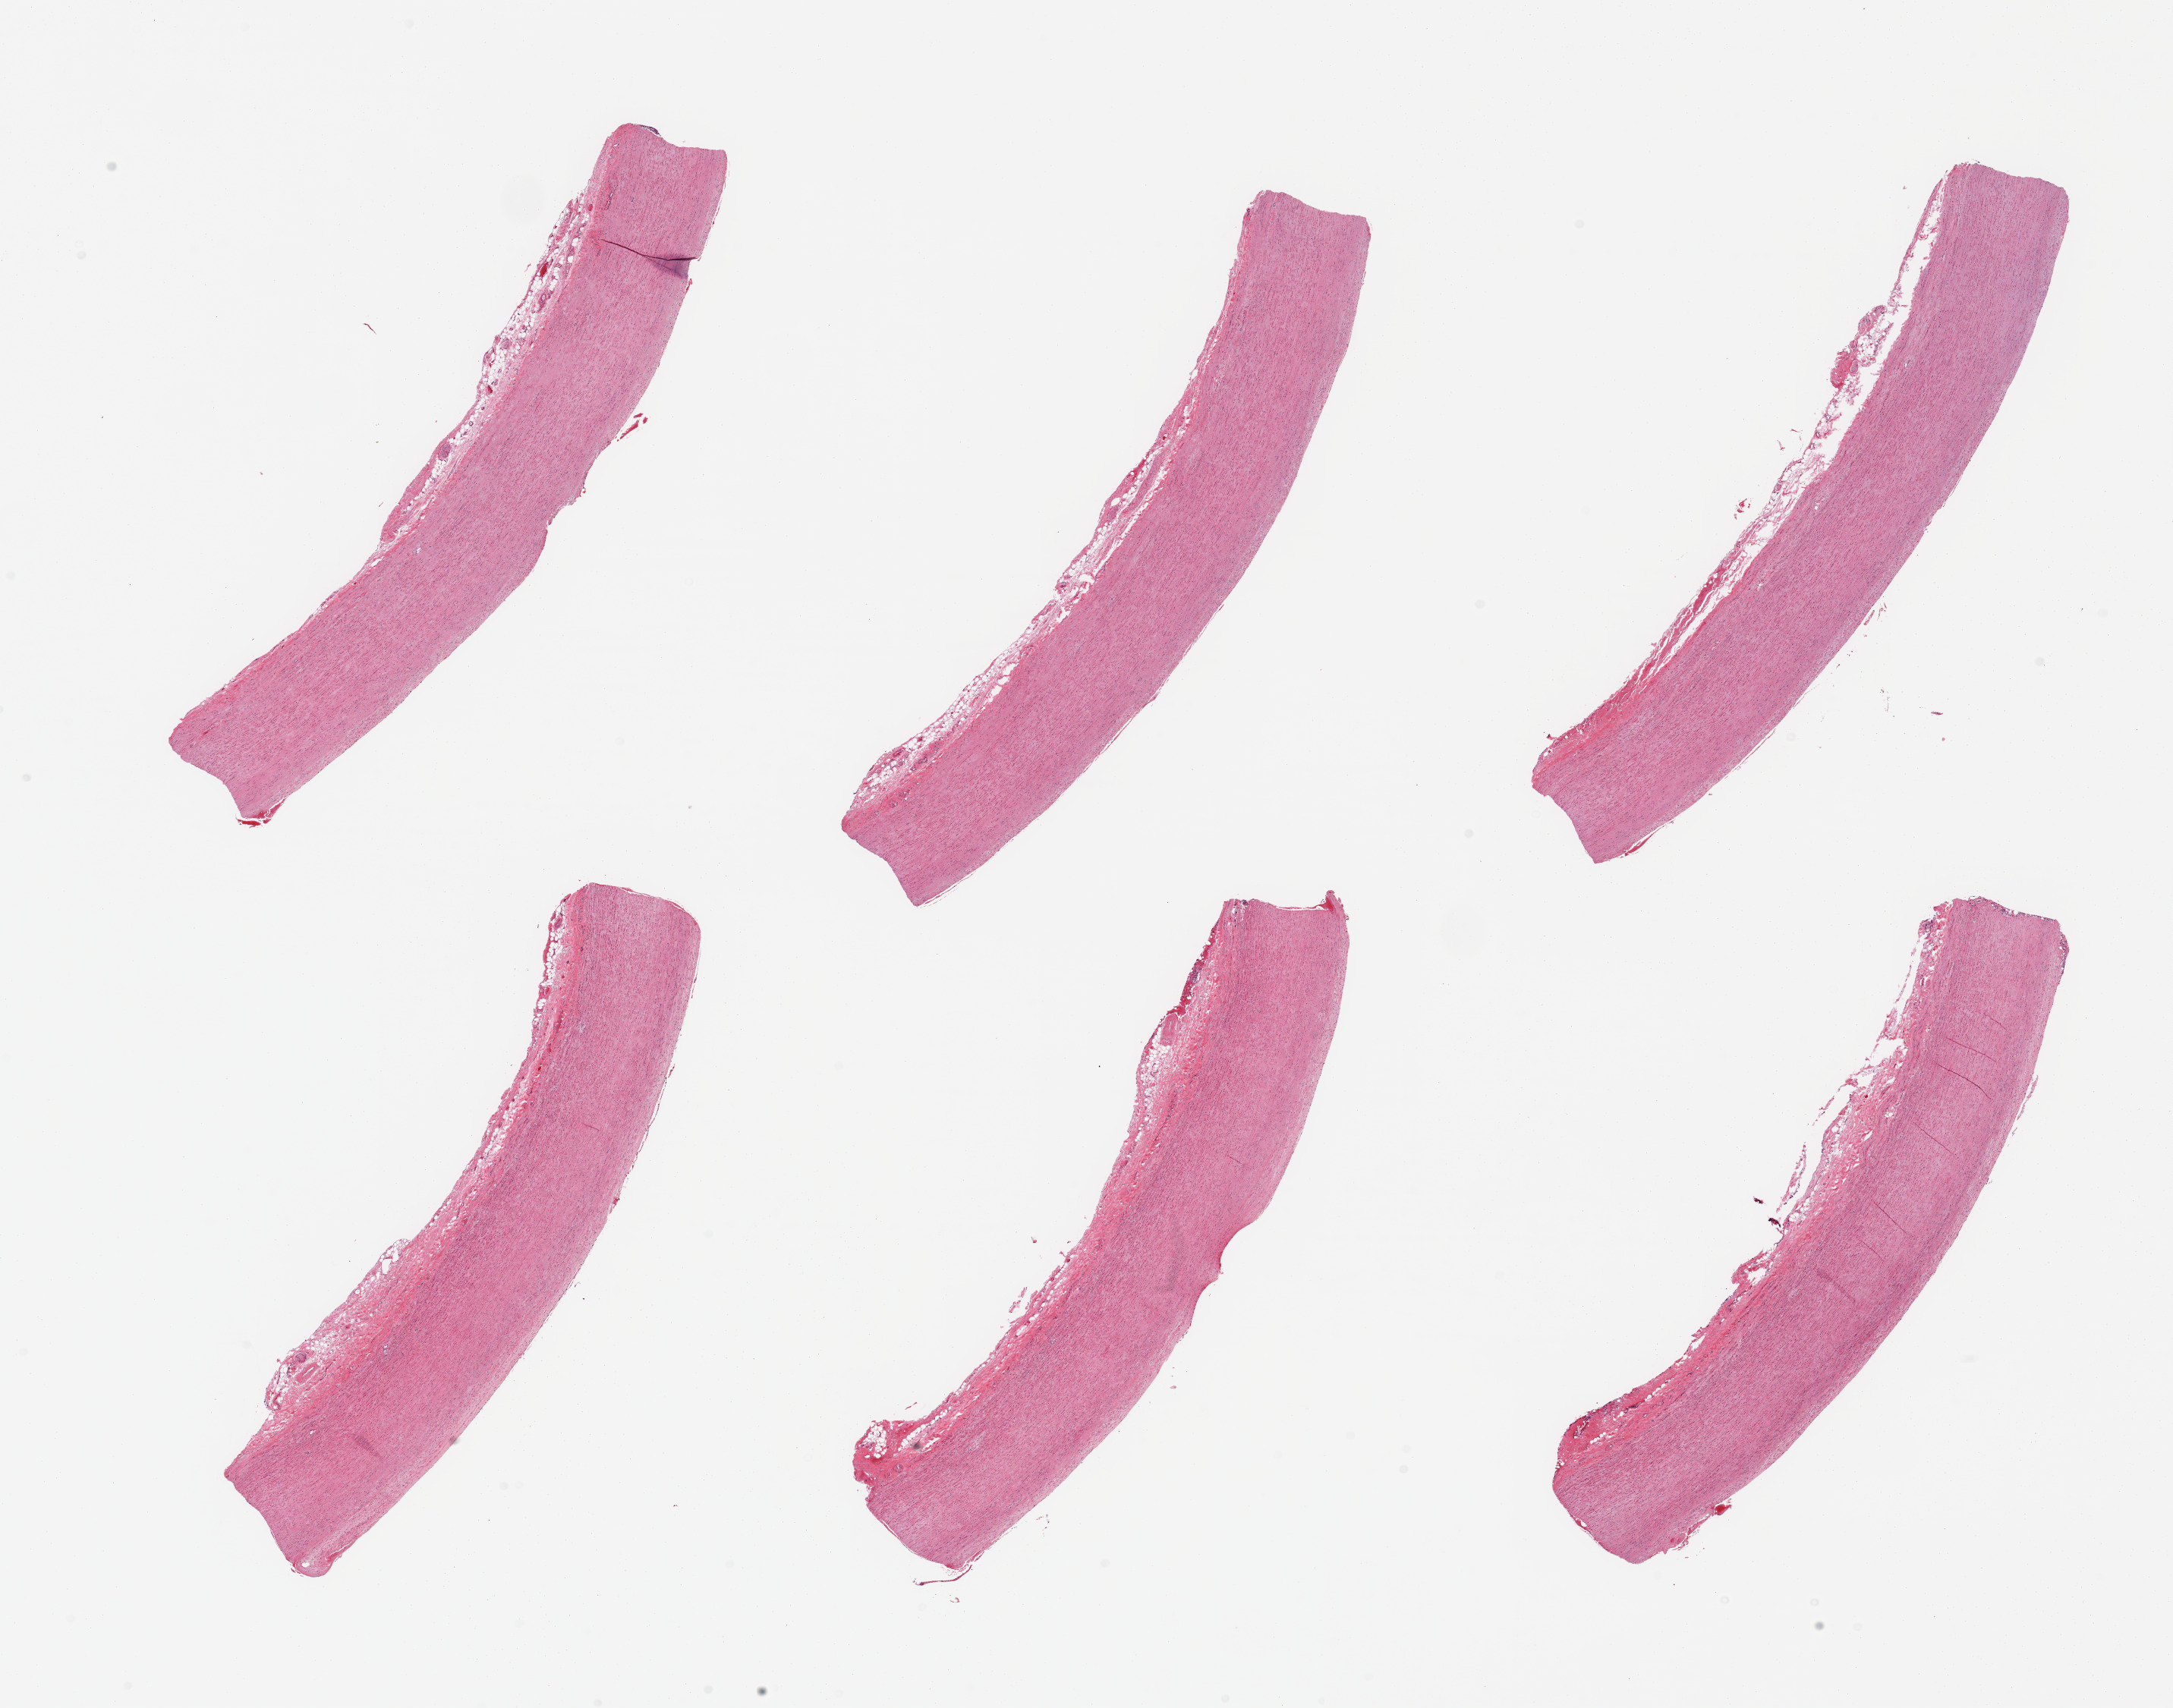
Digitized H&E-stained section, whole scanned area (about 22.6 x 17.8 mm) shown as a low-resolution overview; PAXgene-fixed, paraffin-embedded tissue; target tissue: aorta; tissue donor sample. Male donor.
Reviewer comment on this tissue sample: 6 pieces, minimal atherosis.